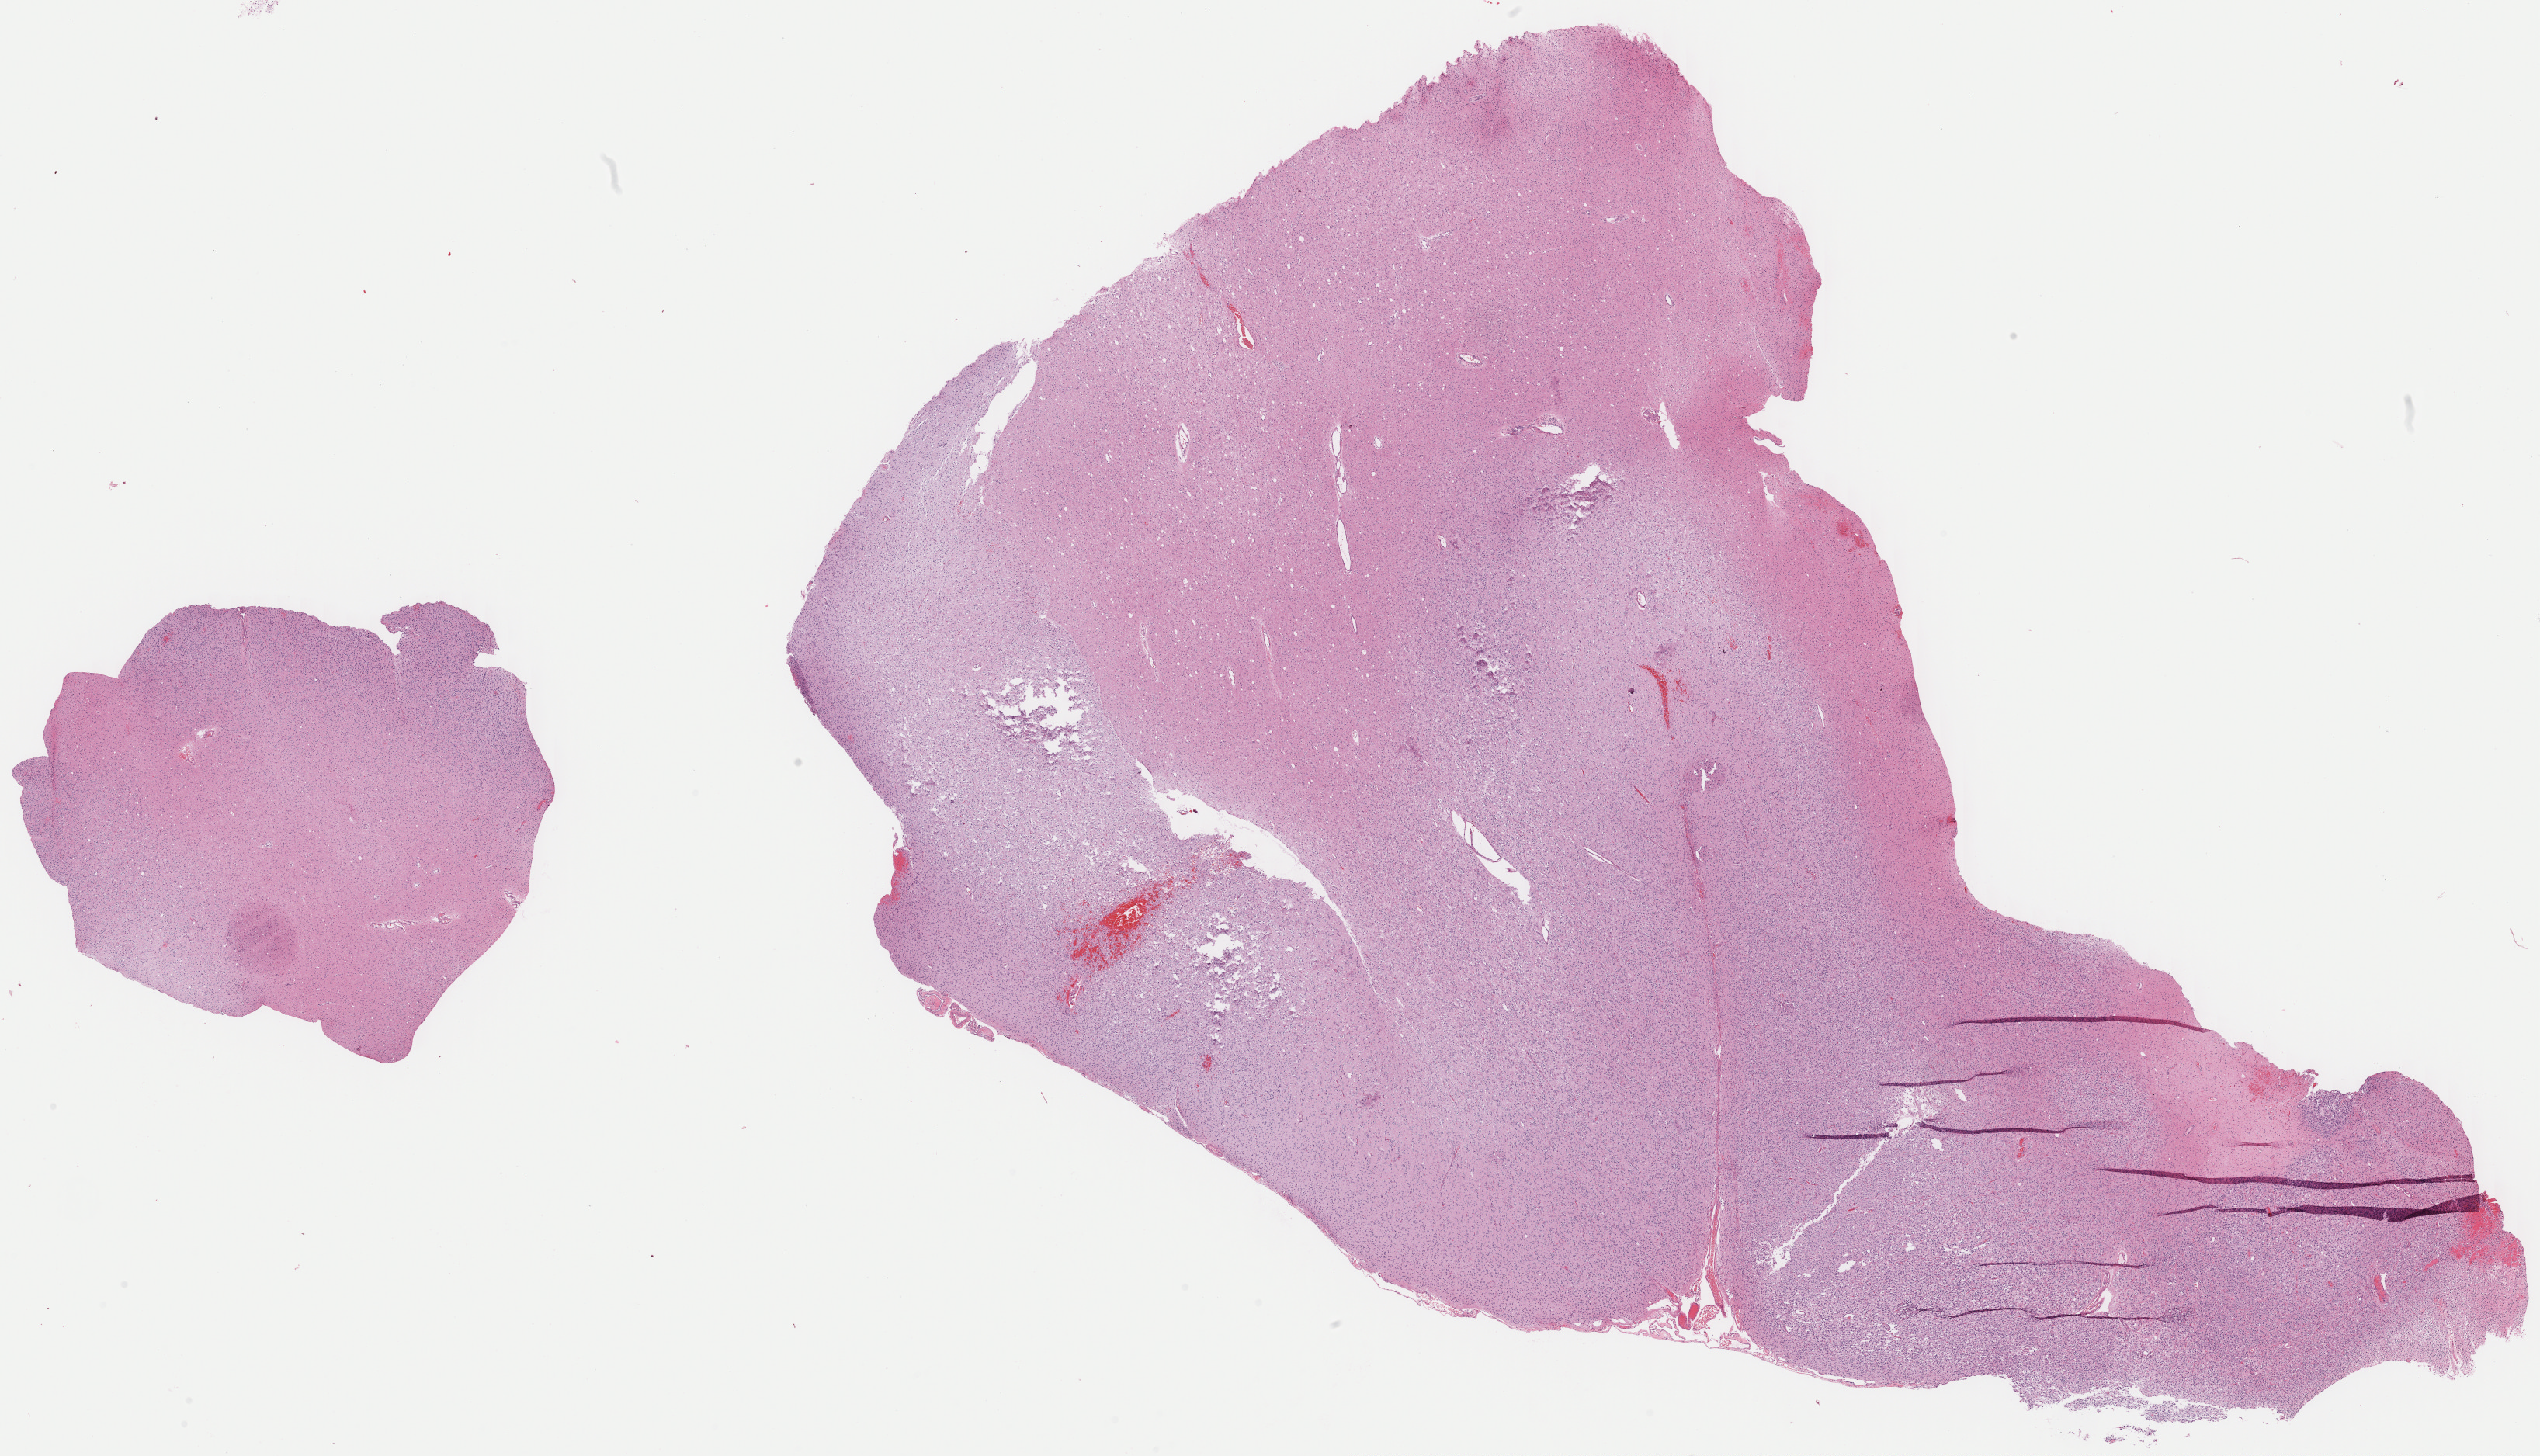
Digitized H&E tissue section (whole slide), whole scanned area (about 25.8 x 14.8 mm, acquisition: 40x scan) shown as a low-resolution overview; formalin-fixed paraffin-embedded (FFPE) diagnostic section; sample: primary tumour, brain. Male patient; age at initial diagnosis 30 years. Histologic grade: G2 (moderately differentiated).
- histologic diagnosis: Mixed glioma (temporal lobe)